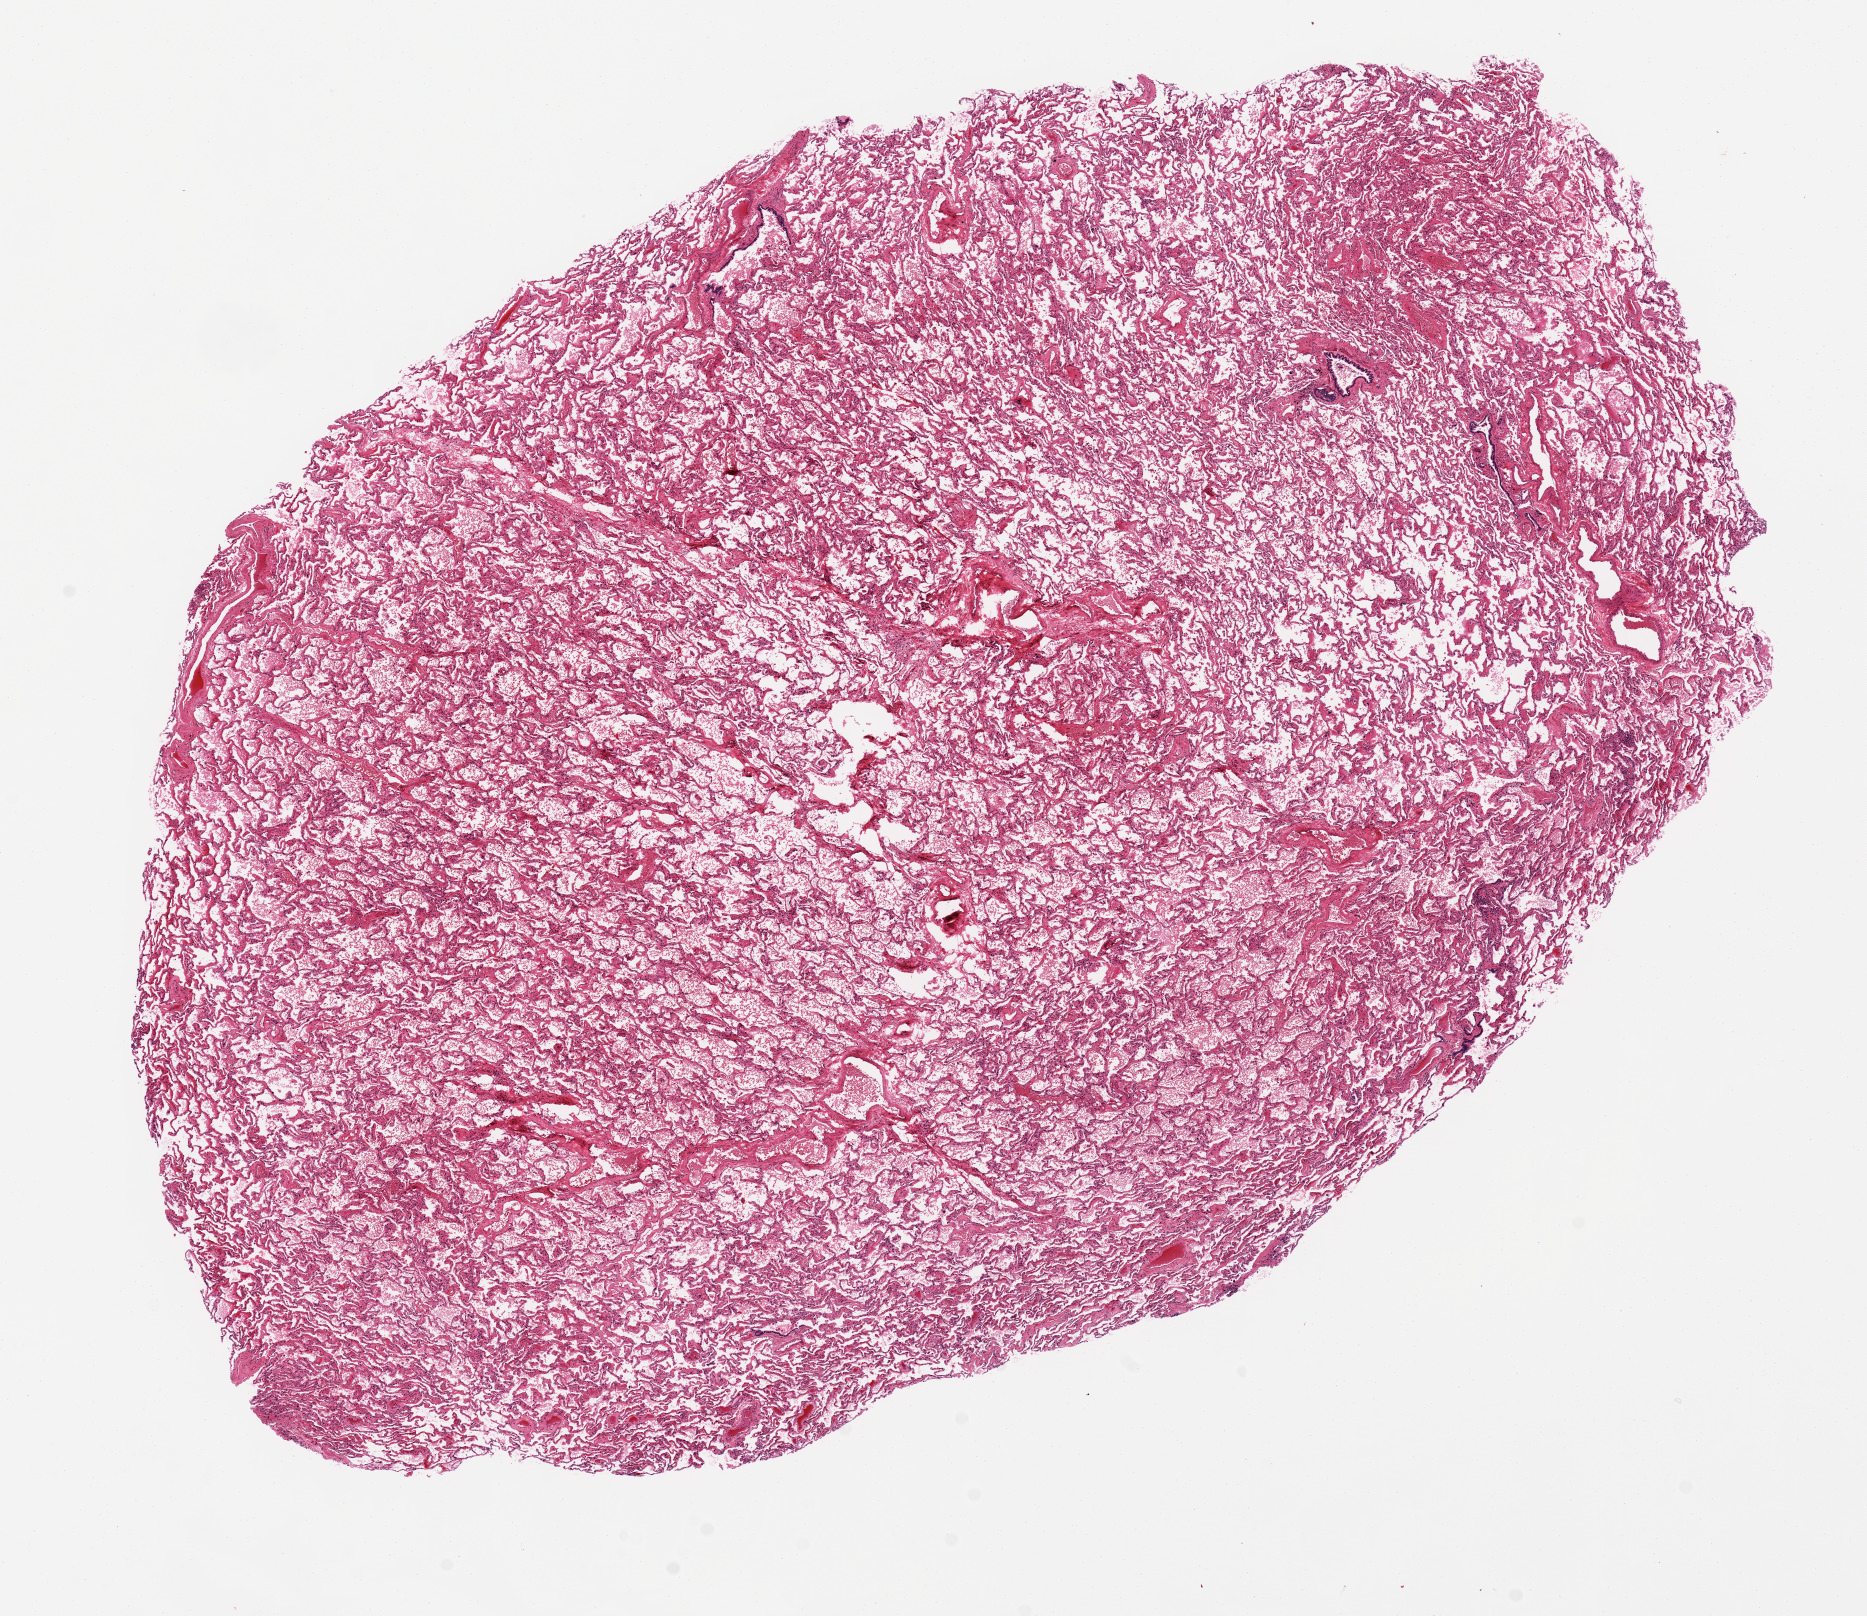
Digitized haematoxylin and eosin-stained section, low-resolution overview of the scanned area, about 14.8 x 12.8 mm. PAXgene-fixed paraffin-embedded (PFPE) section. Target tissue: lung. Tissue donor sample. Donor: male.
Pathologist's review note for this sample: 9 x 14mm. Diffuse mild edema.